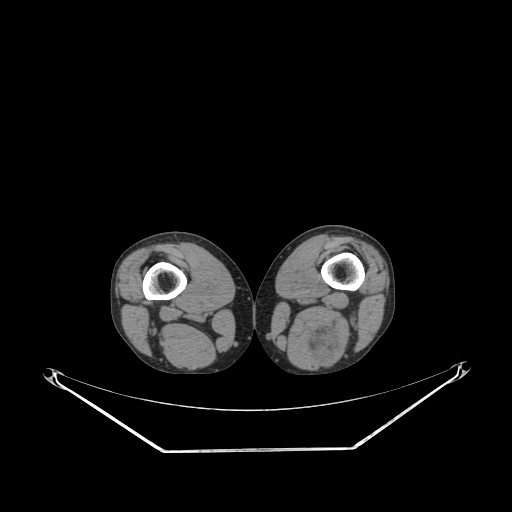
CT of an extremity soft-tissue mass (from a PET/CT study), one axial slice; slice 200 of 267 in the series (ordered by position); reconstruction kernel SOFT; 140 kVp; soft-tissue window (W 400 / L 40 HU); 3.75 mm slice thickness; 512 × 512 image matrix, field of view 500 × 500 mm. Male patient. Case-level facts recorded for this patient, not image findings: histological type: synovial sarcoma; site of the primary tumour: left poplietal fossa.
Outlined on this slice (expert contour drawn on MRI and transferred to this co-registered scan by the dataset authors):
- gross tumour volume (mass): bounding box (x1, y1, x2, y2) in pixels: (306, 326, 339, 364)